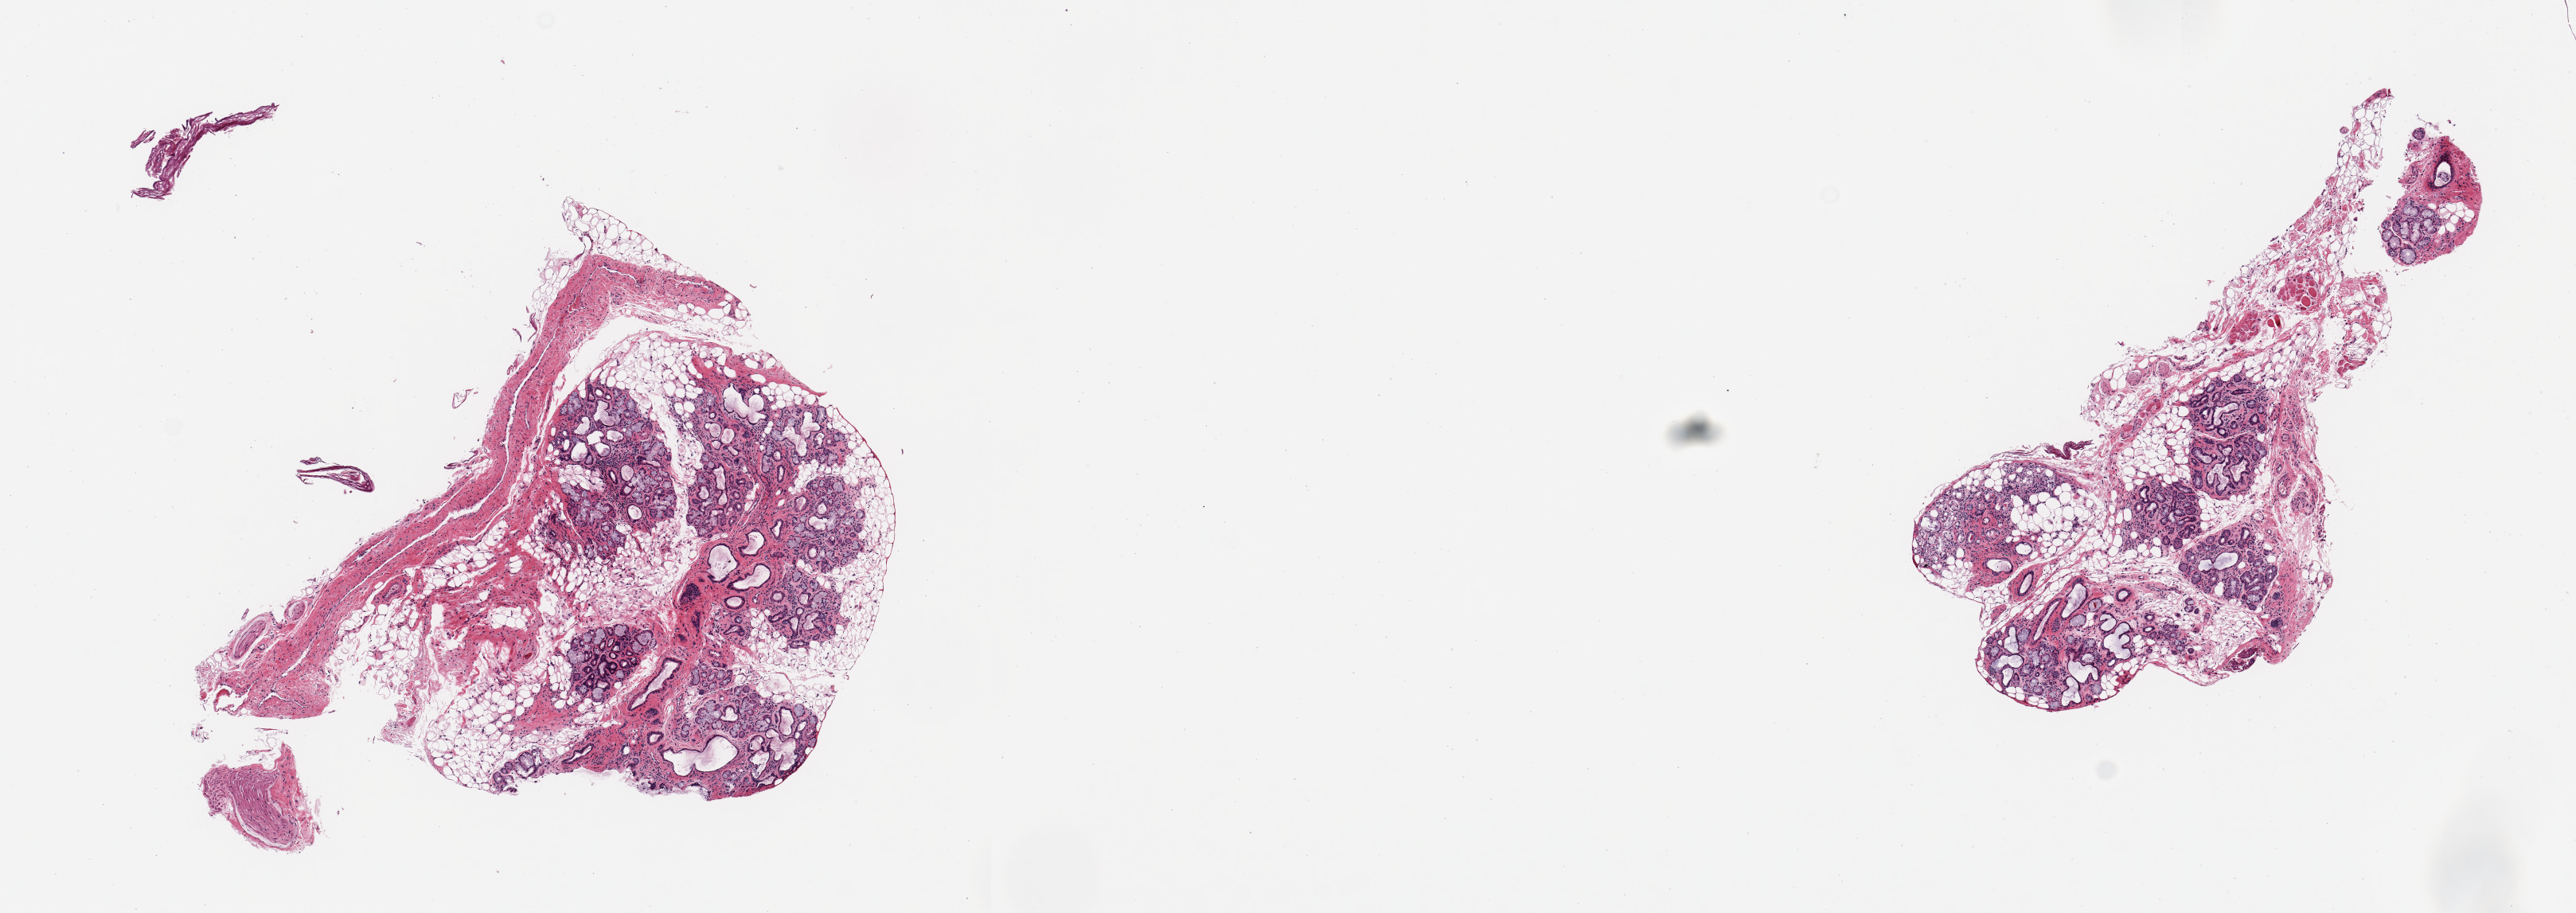
Digitized H&E-stained section, a low-resolution overview of the entire scanned area, about 12.8 x 4.5 mm (slide scanned at 20x); PAXgene-fixed paraffin-embedded (PFPE) section; sampled site (target tissue): minor salivary gland; donor tissue sample.
Review note (as recorded): 2 pieces, ~50% glandular elements, rest is fat/connetive tissue.